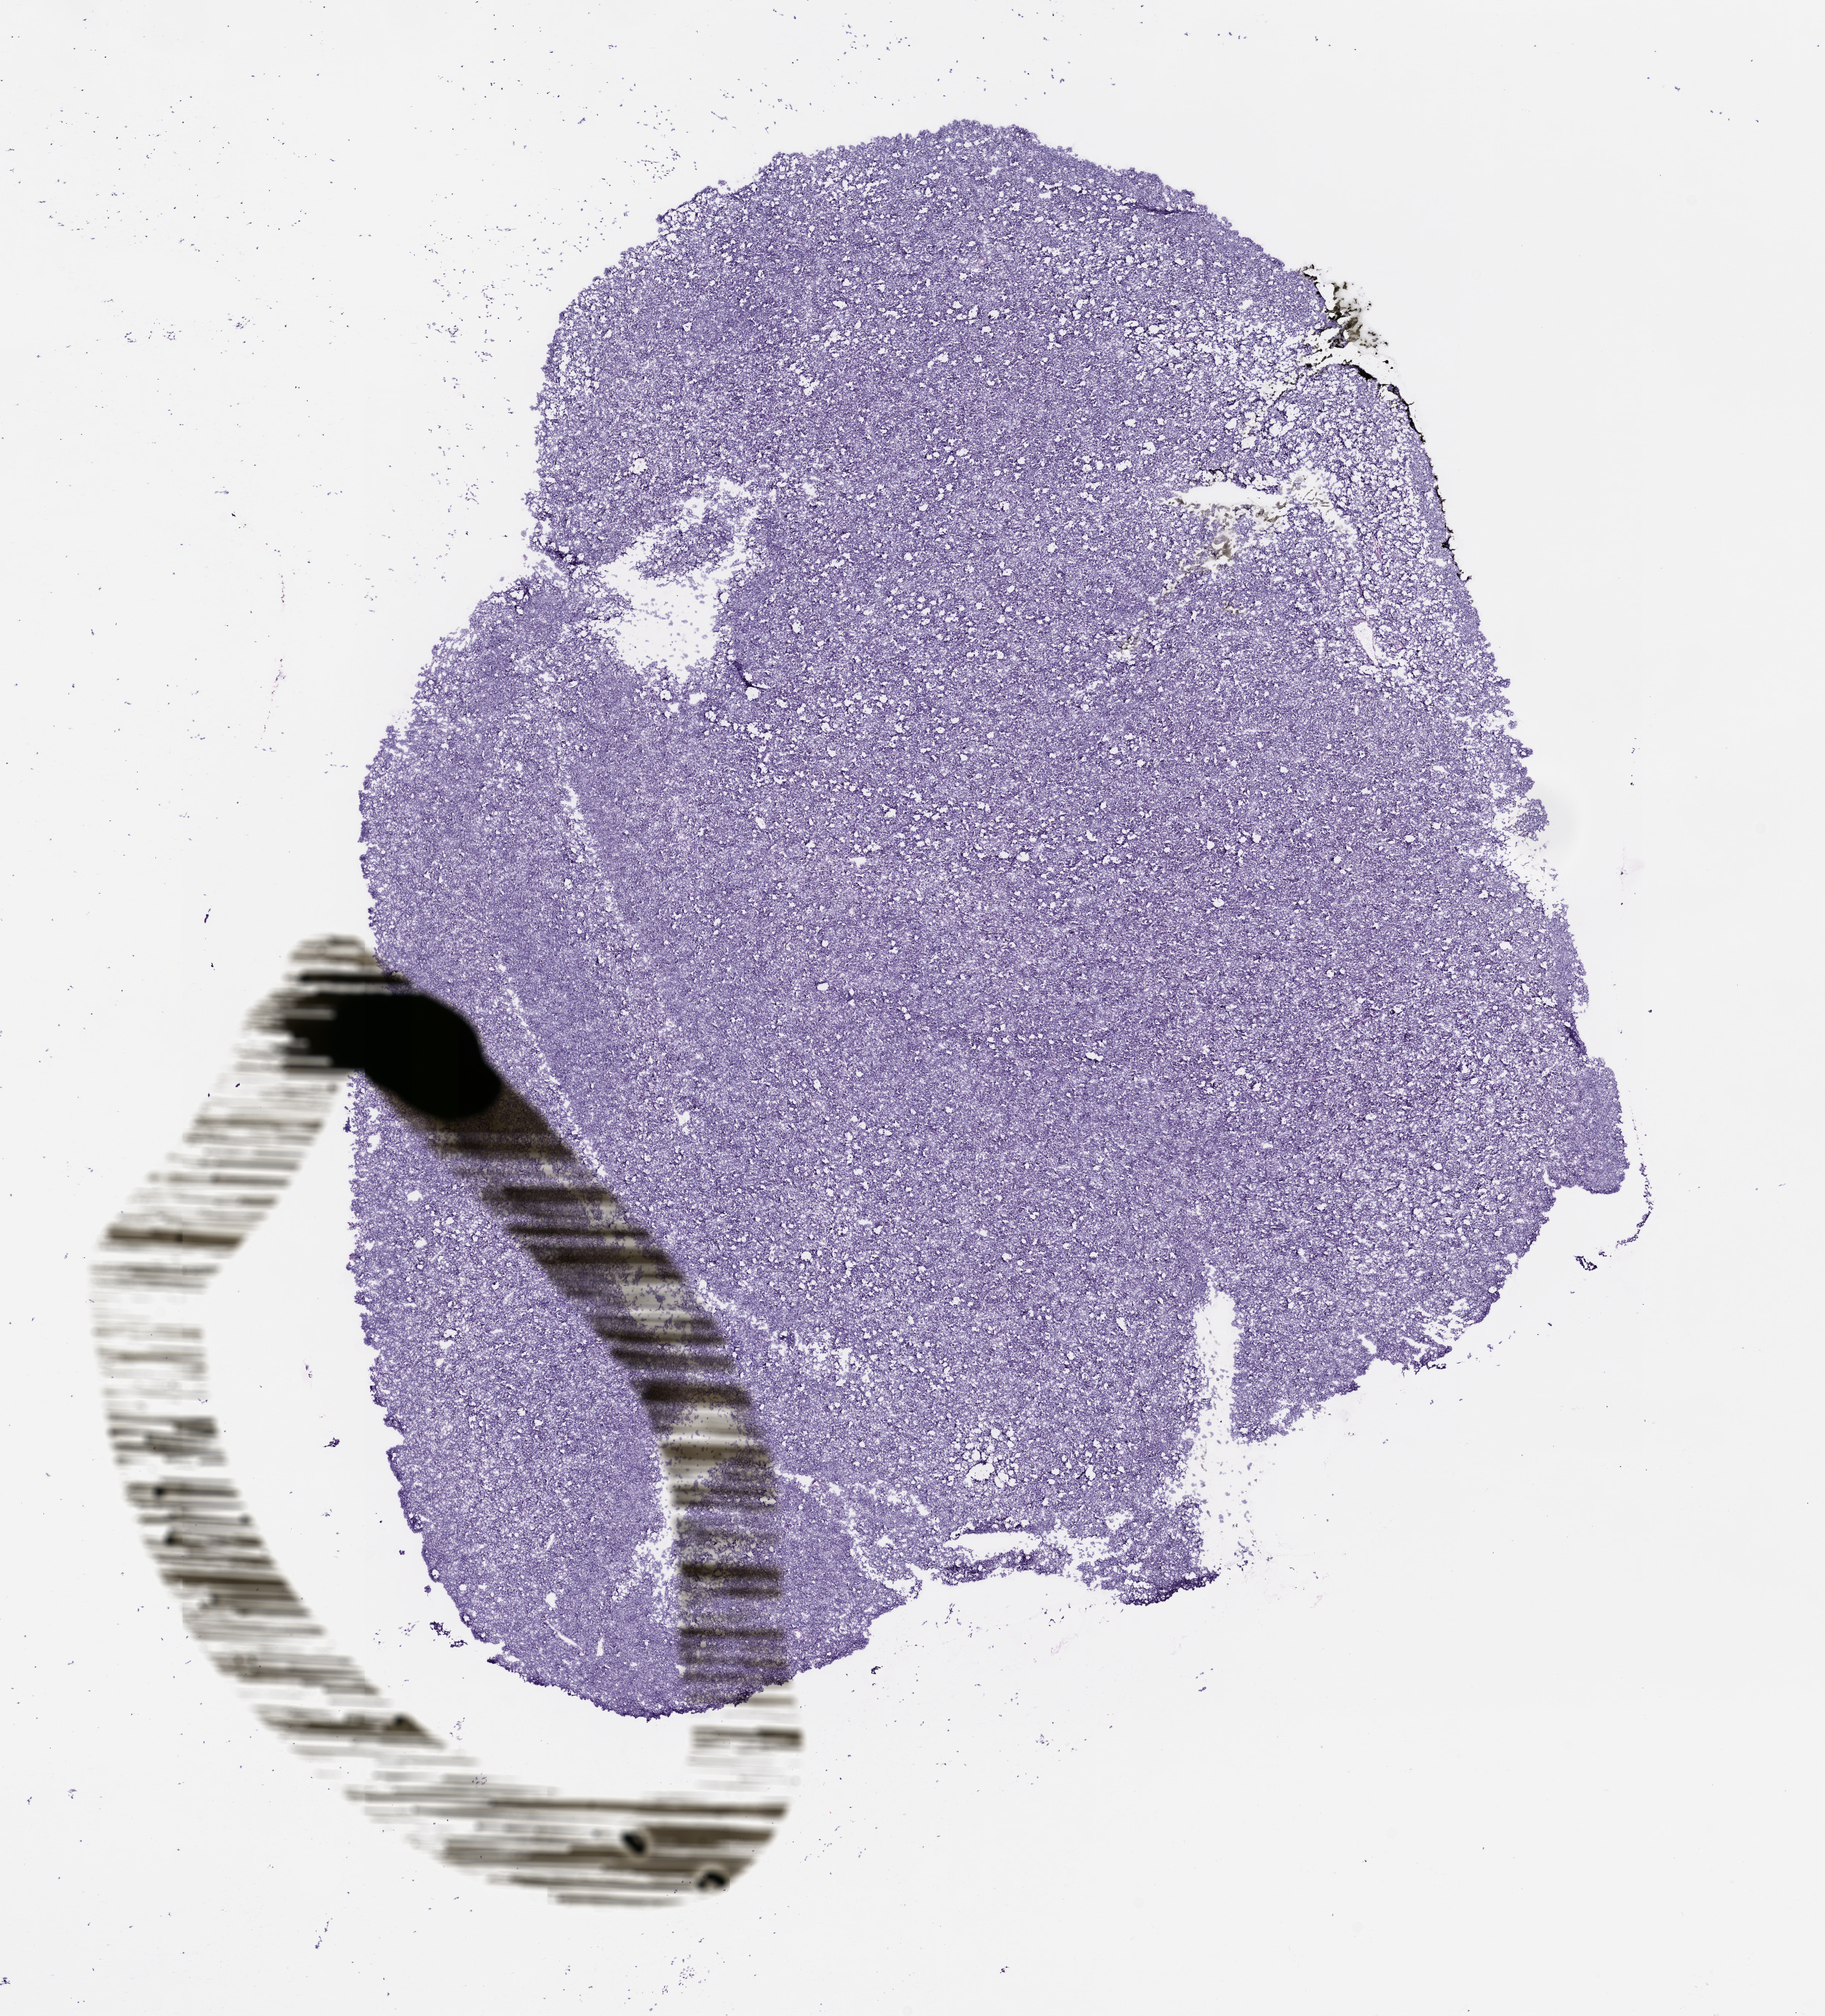
Haematoxylin and eosin whole-slide image of a patient-derived xenograft (PDX) tumor grown in a mouse, passage 1 — shown as a low-resolution overview of the whole scanned area (about 10.0 x 11.1 mm); FFPE section; originating tumor site category: musculoskeletal.
* originating patient diagnosis: Synovial Sarcoma